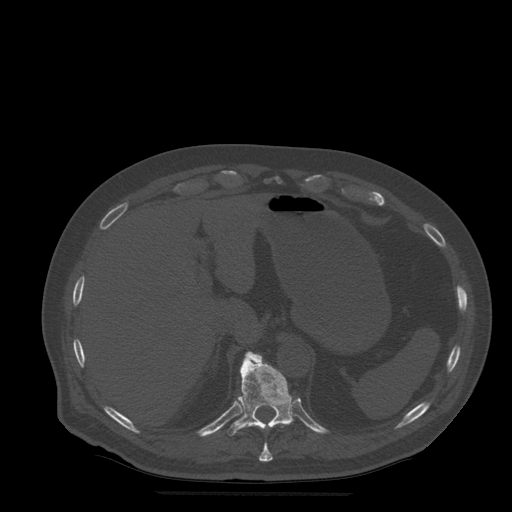
CT including the spine, one axial slice; position 251 of 522 along the scan axis; bone window (W 1800 / L 400 HU); 1.25 mm slice thickness; 512 × 512 image matrix, field of view 420 × 420 mm. Patient age 72 years. From the clinical record (not read from this slice): primary cancer: prostate.
Outlined on this slice (semi-automatic segmentation, software-assisted and operator-edited):
- T10 vertebra: bounding box <253,425,273,462> (left, top, right, bottom; pixels)
- T11 vertebra: <228,352,296,436>